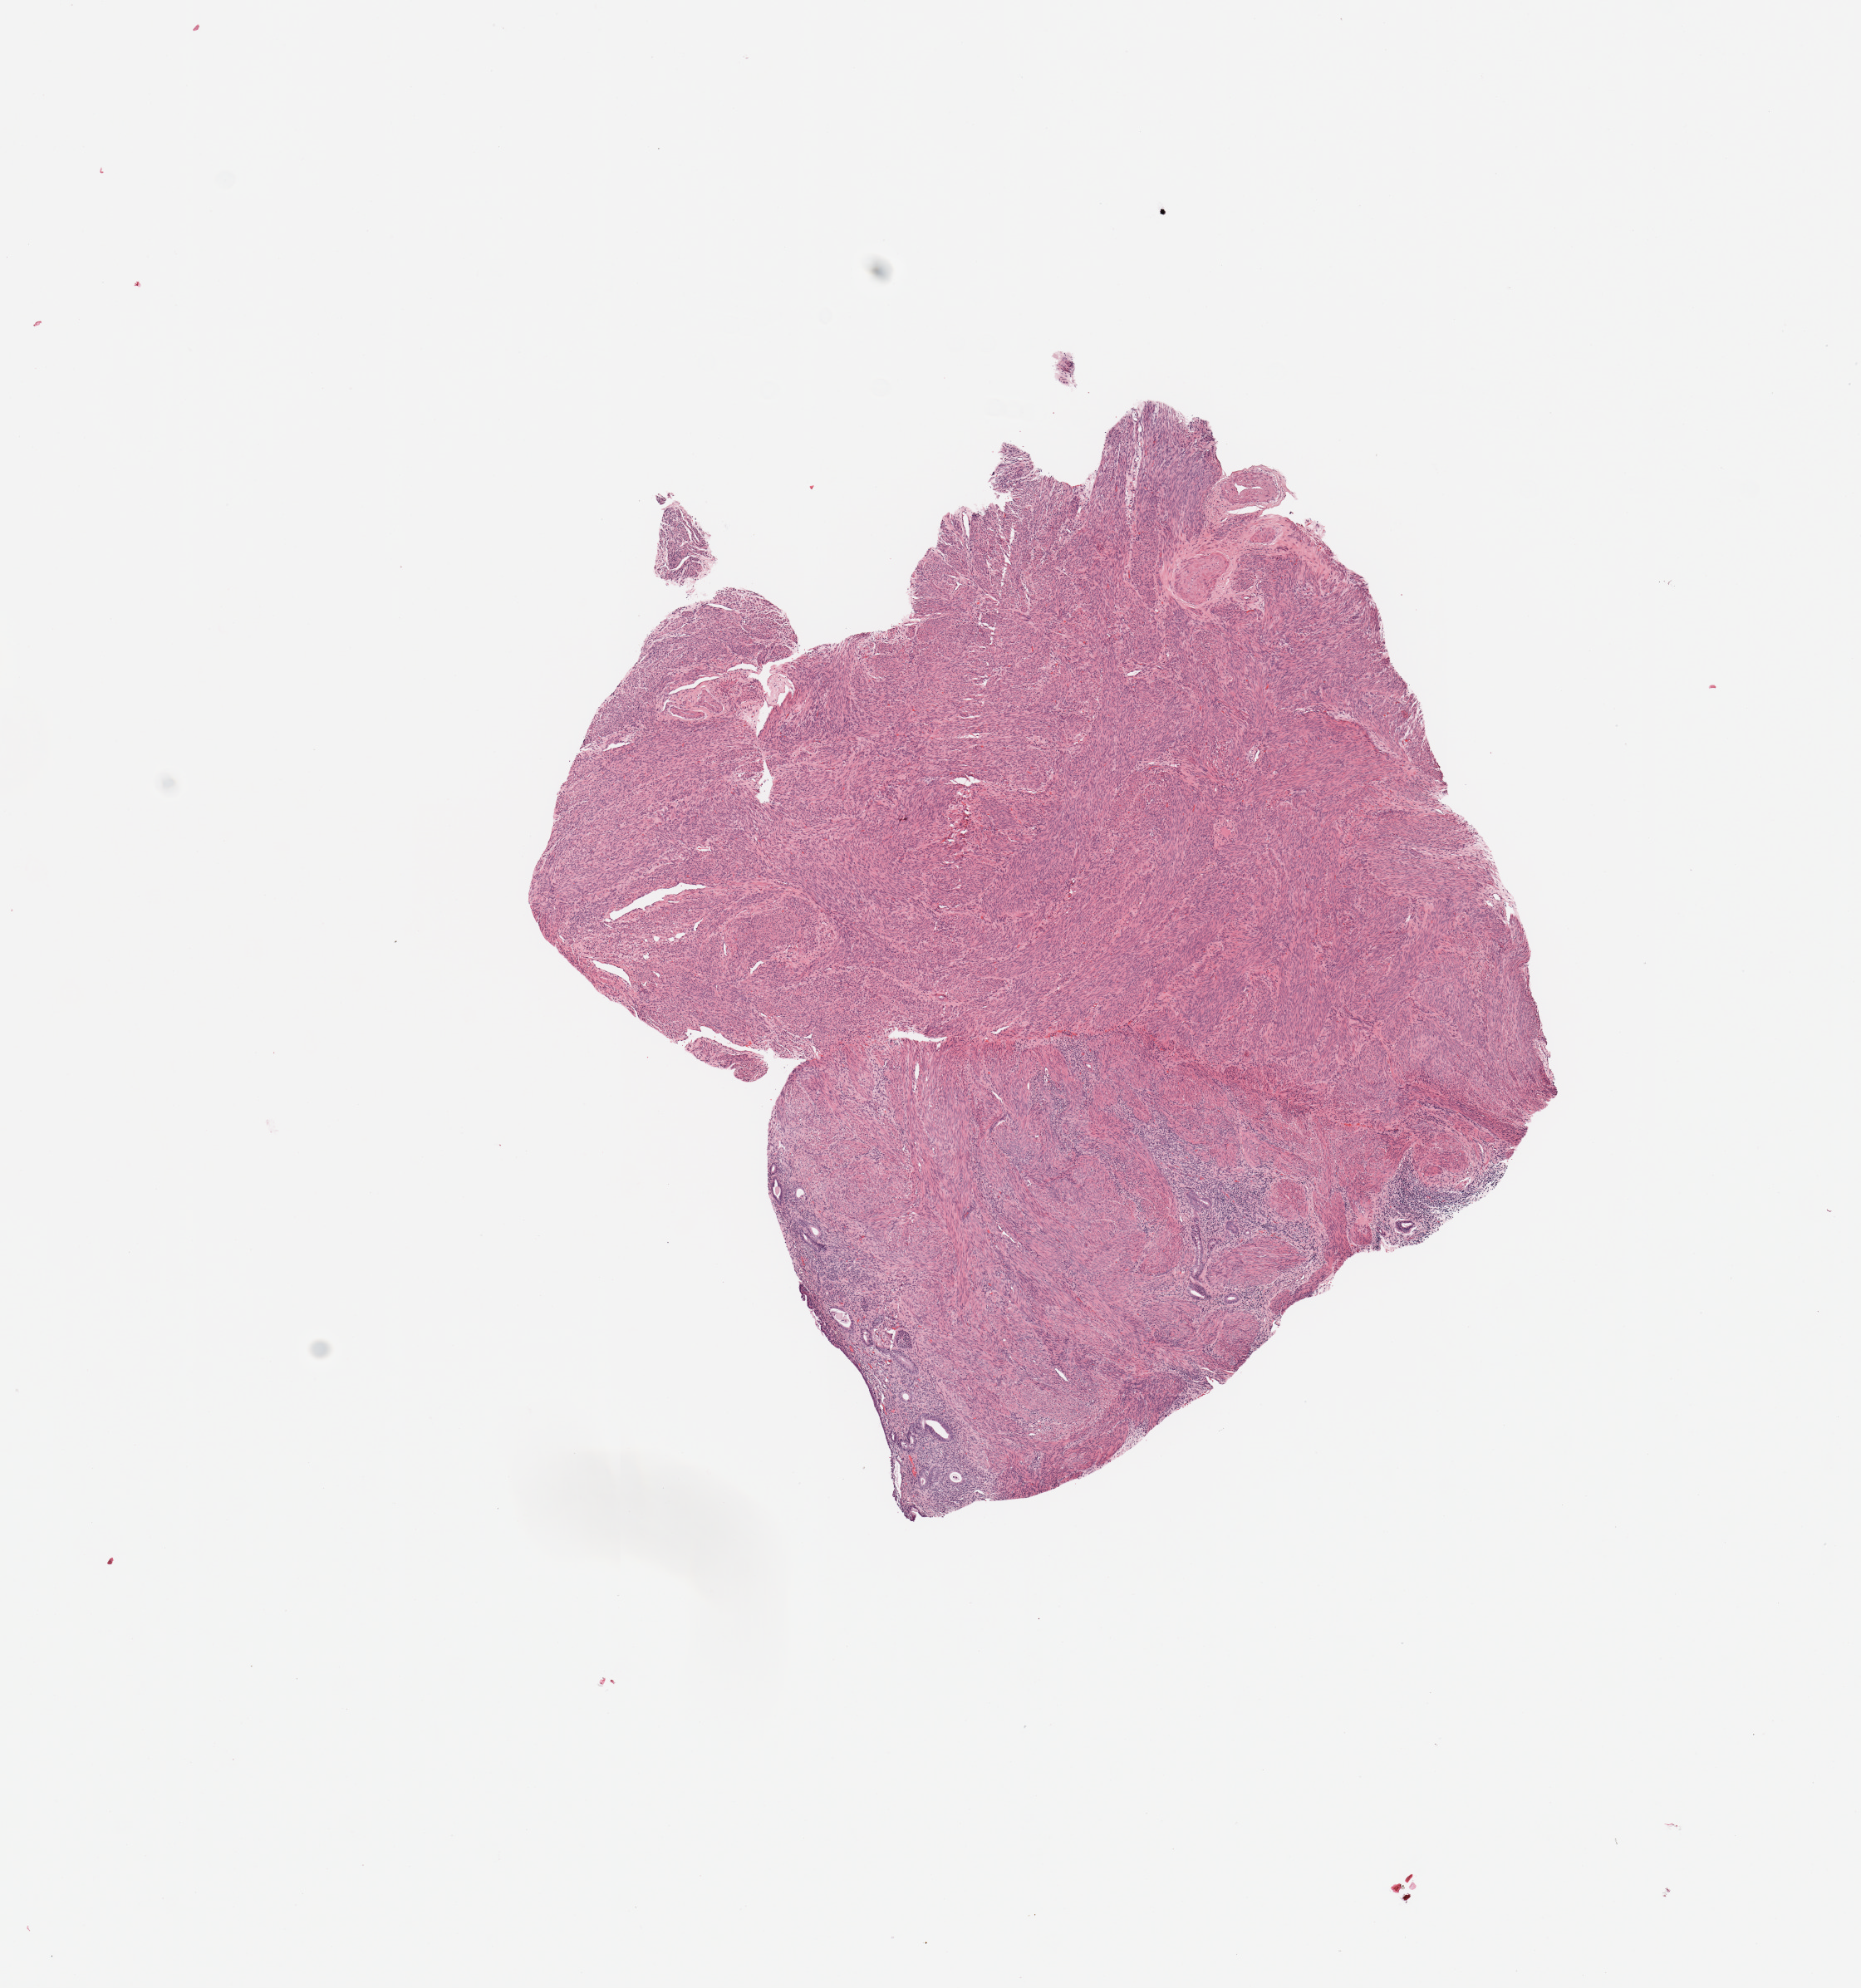
Whole-slide histology image, H&E-stained, whole scanned area (about 8.9 x 9.5 mm, slide scanned at 20x) shown as a low-resolution overview; normal (non-tumour) tissue sample, uterus. Female, 71 y/o.
This section: normal (non-tumour) tissue from the same patient. Patient diagnosis: Endometrioid adenocarcinoma, NOS.